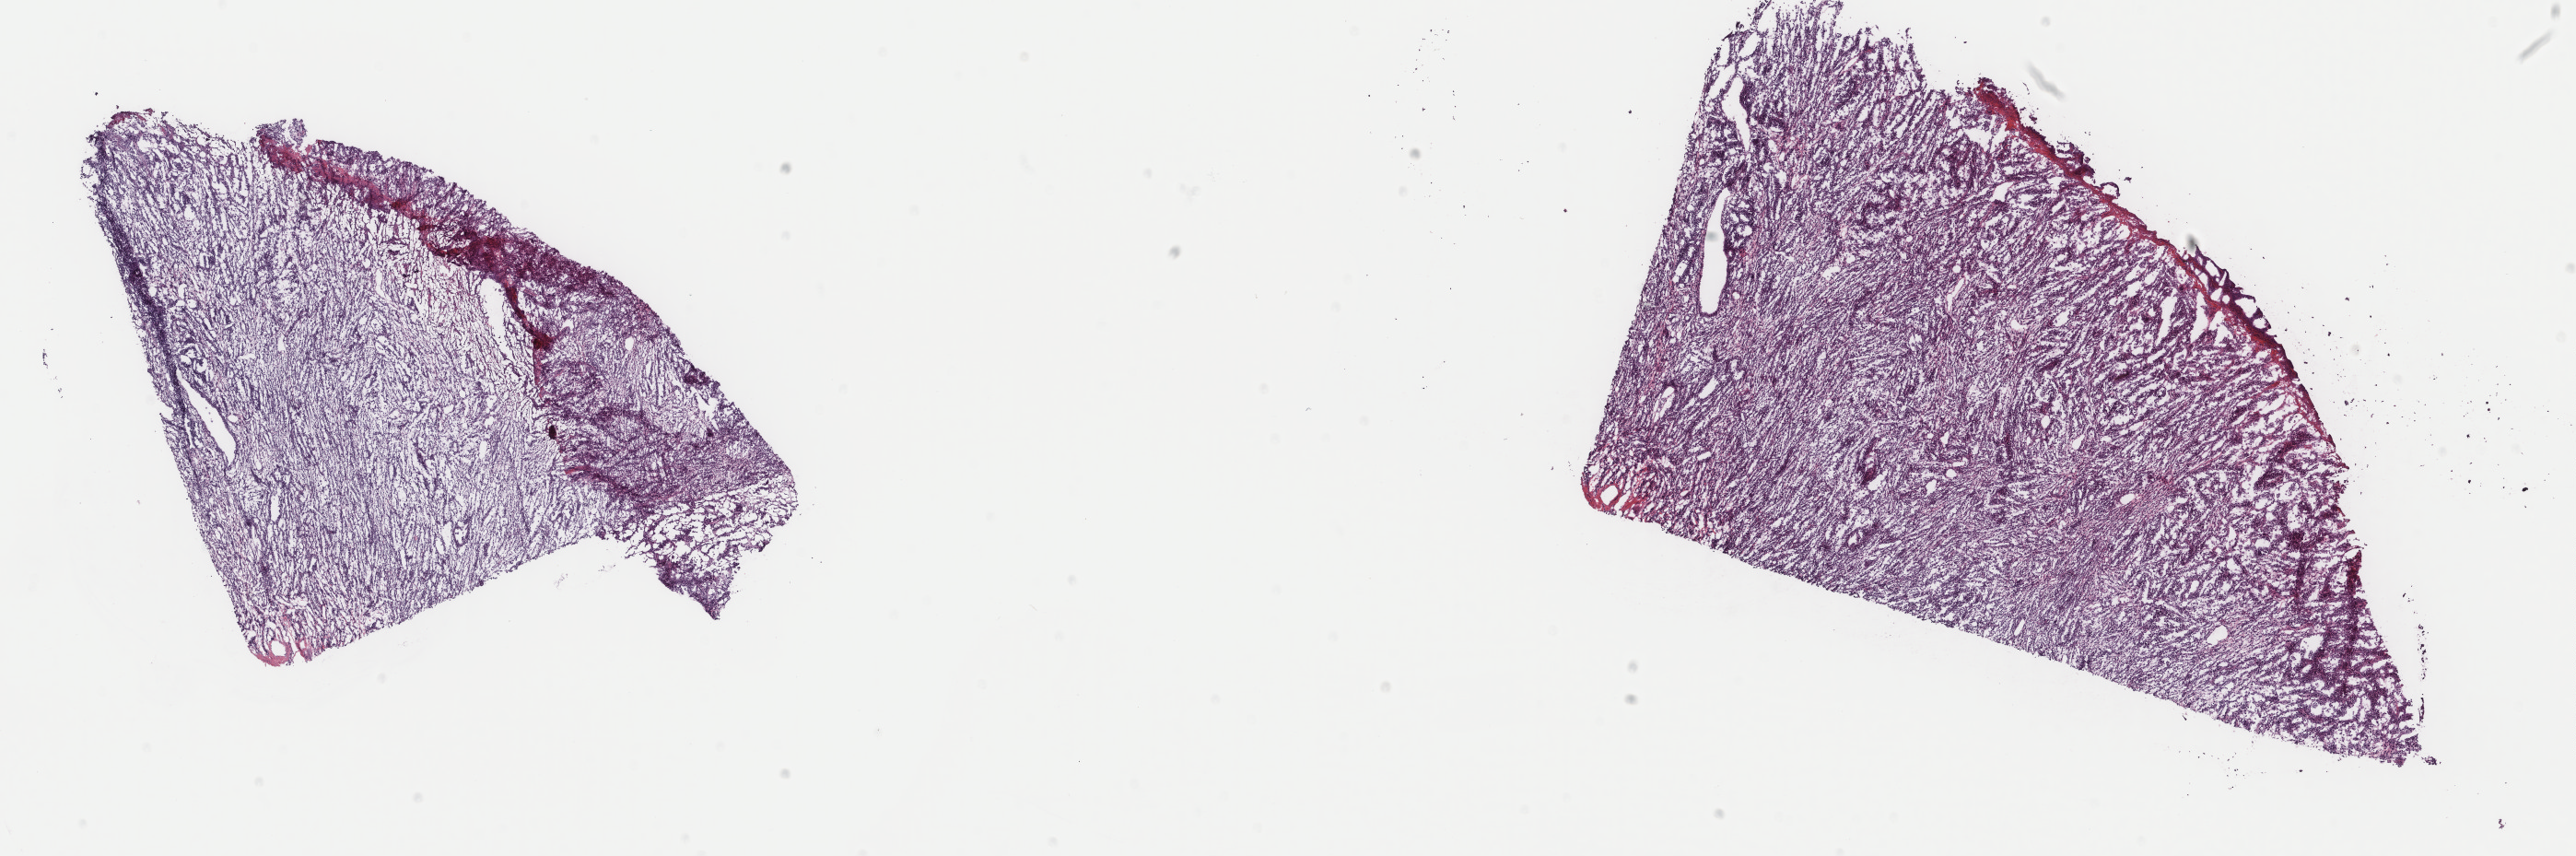
Digitized H&E tissue section (whole slide) — whole scanned area (about 22.2 x 7.4 mm) shown as a low-resolution overview; frozen section from the top of the tissue portion; primary tumour sample from the skin. Male patient; age at initial diagnosis 82 years. Composition of this section per pathologist review: tumour cells 98%, tumour nuclei 85%, normal cells 0%, stromal cells 0%, necrosis 2%. Inflammatory infiltration, as recorded: lymphocyte infiltration 1%, monocyte infiltration 0%, neutrophil infiltration 0%.
AJCC pathologic stage: IIC (7th edition). TNM: T4b N0 M0. Histologic diagnosis: Amelanotic melanoma.